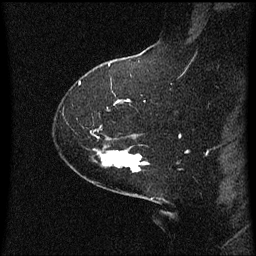
Breast MRI (dynamic contrast-enhanced), one sagittal slice; position 44 of 60 along the scan axis; dynamic contrast-enhanced series, image 2 of 3 at this slice position (ordered by acquisition); 1.5 T; TE 4.2 ms, TR 8 ms; 2.1 mm slice thickness; 256 × 256 image matrix, field of view 200 × 200 mm. Patient: female, 59 years.
Annotated regions visible in this slice (semi-automatic segmentation, software-assisted and operator-edited):
- analysis volume of interest (the breast-tissue region the enhancement analysis was run in; not a lesion): bounding box <94,146,149,173> (left, top, right, bottom; pixels)
- tumour enhancement mask (voxels above the 70 % enhancement threshold inside the analysis volume of interest): <130,162,145,169>